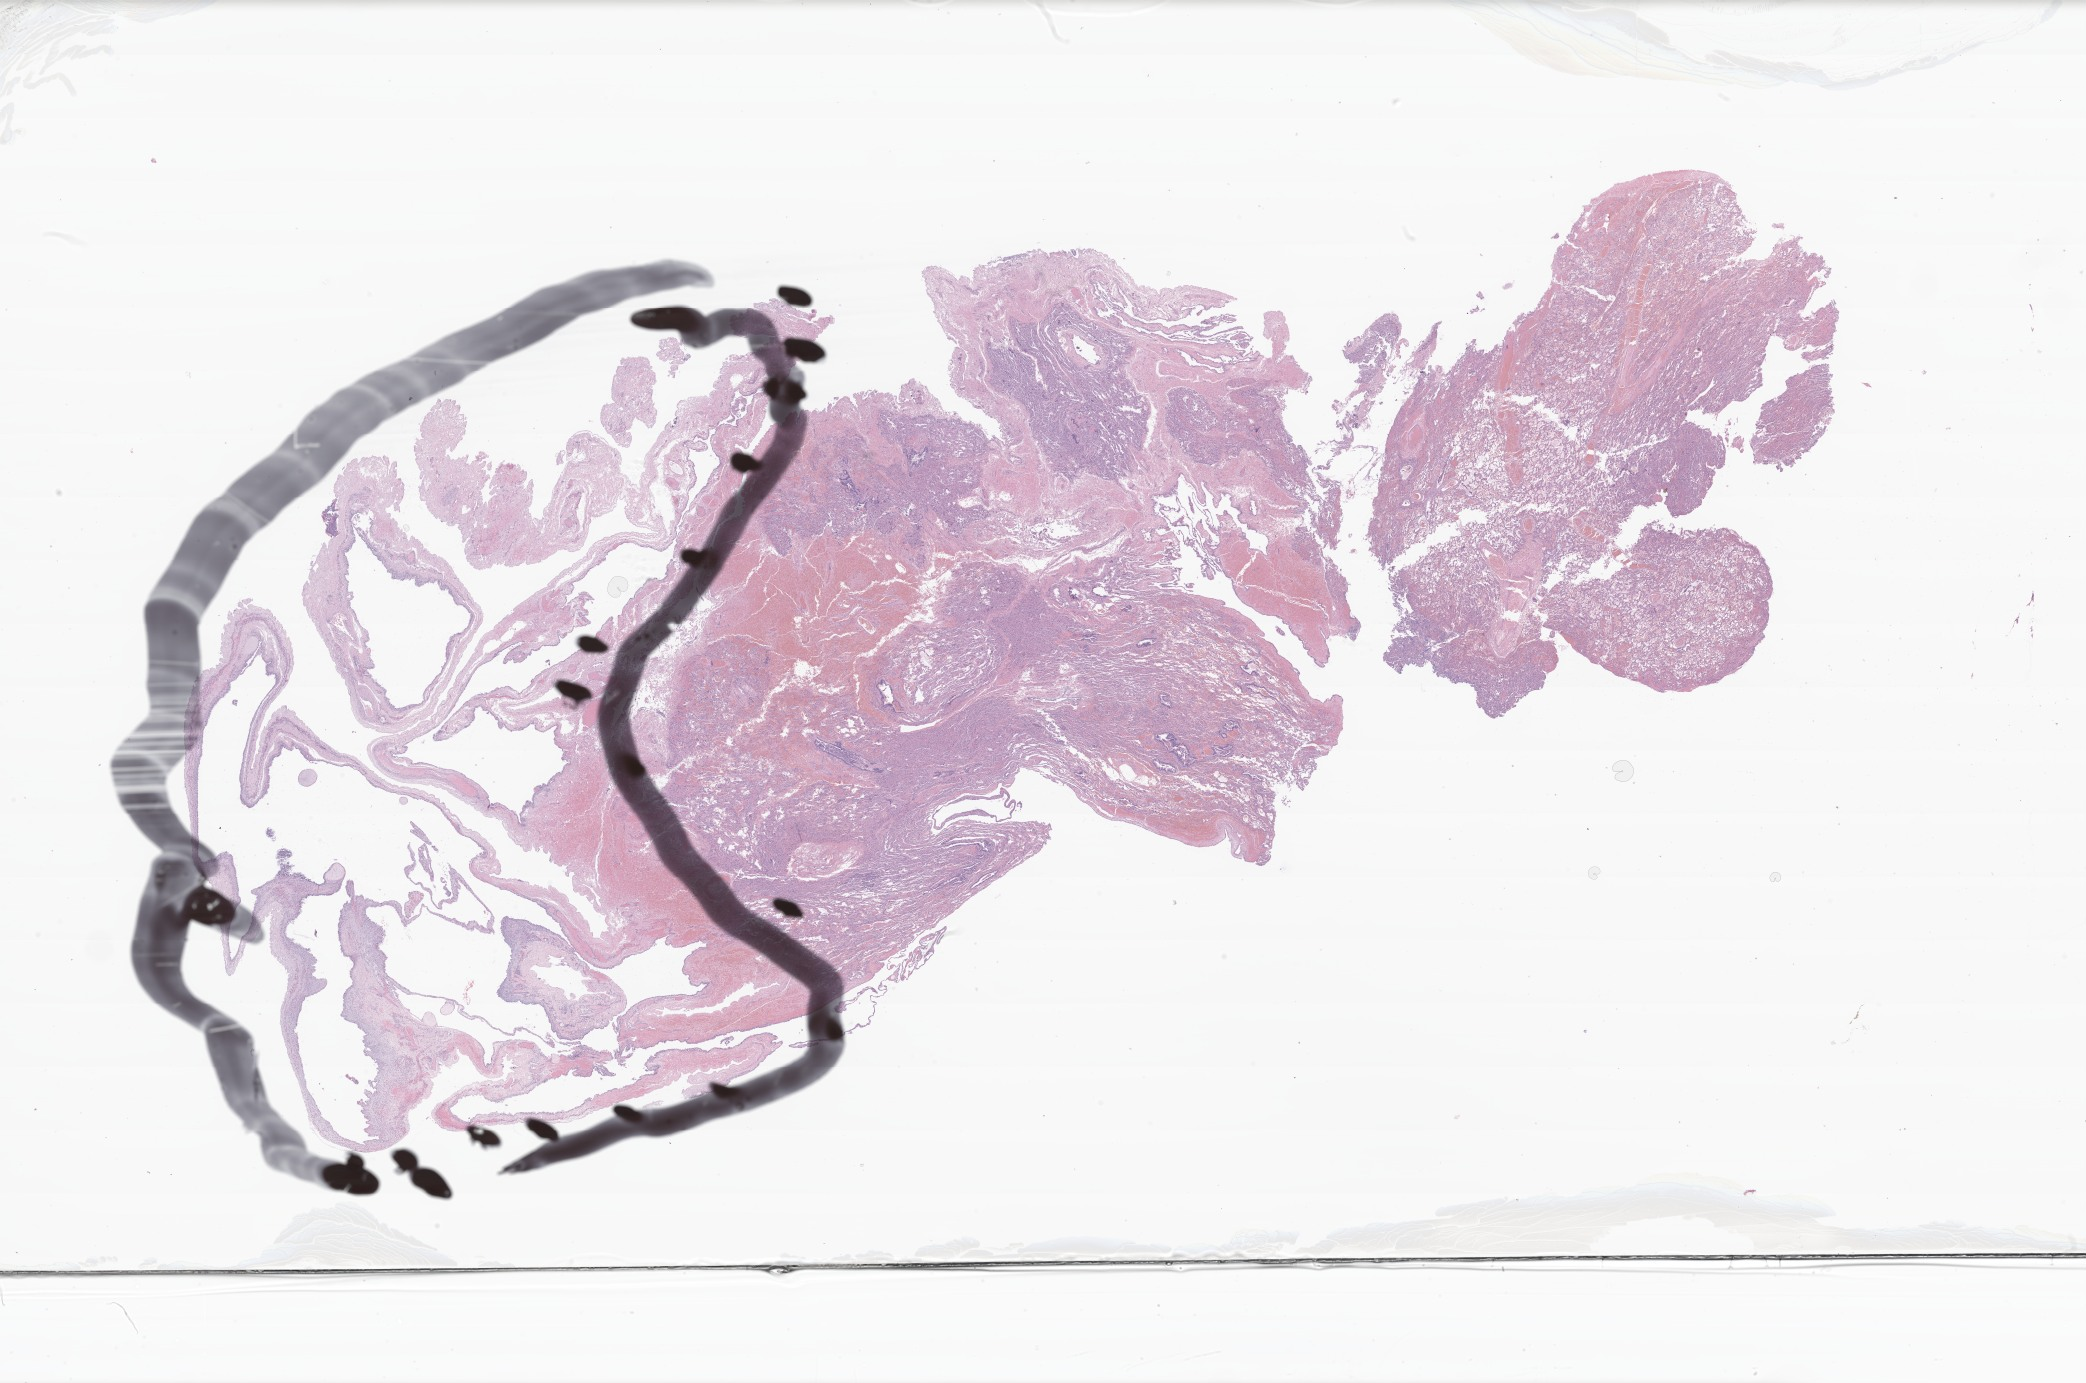
Hematoxylin and eosin (H&E) whole-slide image of tumor tissue from the lower lobe of lung — low-resolution overview of the scanned area, about 35.1 x 23.3 mm, formalin-fixed paraffin-embedded section. Female patient, age 755 days (about 2.1 years).
Recorded diagnosis: Pleuropulmonary blastoma. Tissue or organ of origin (case record): lower lobe, lung.